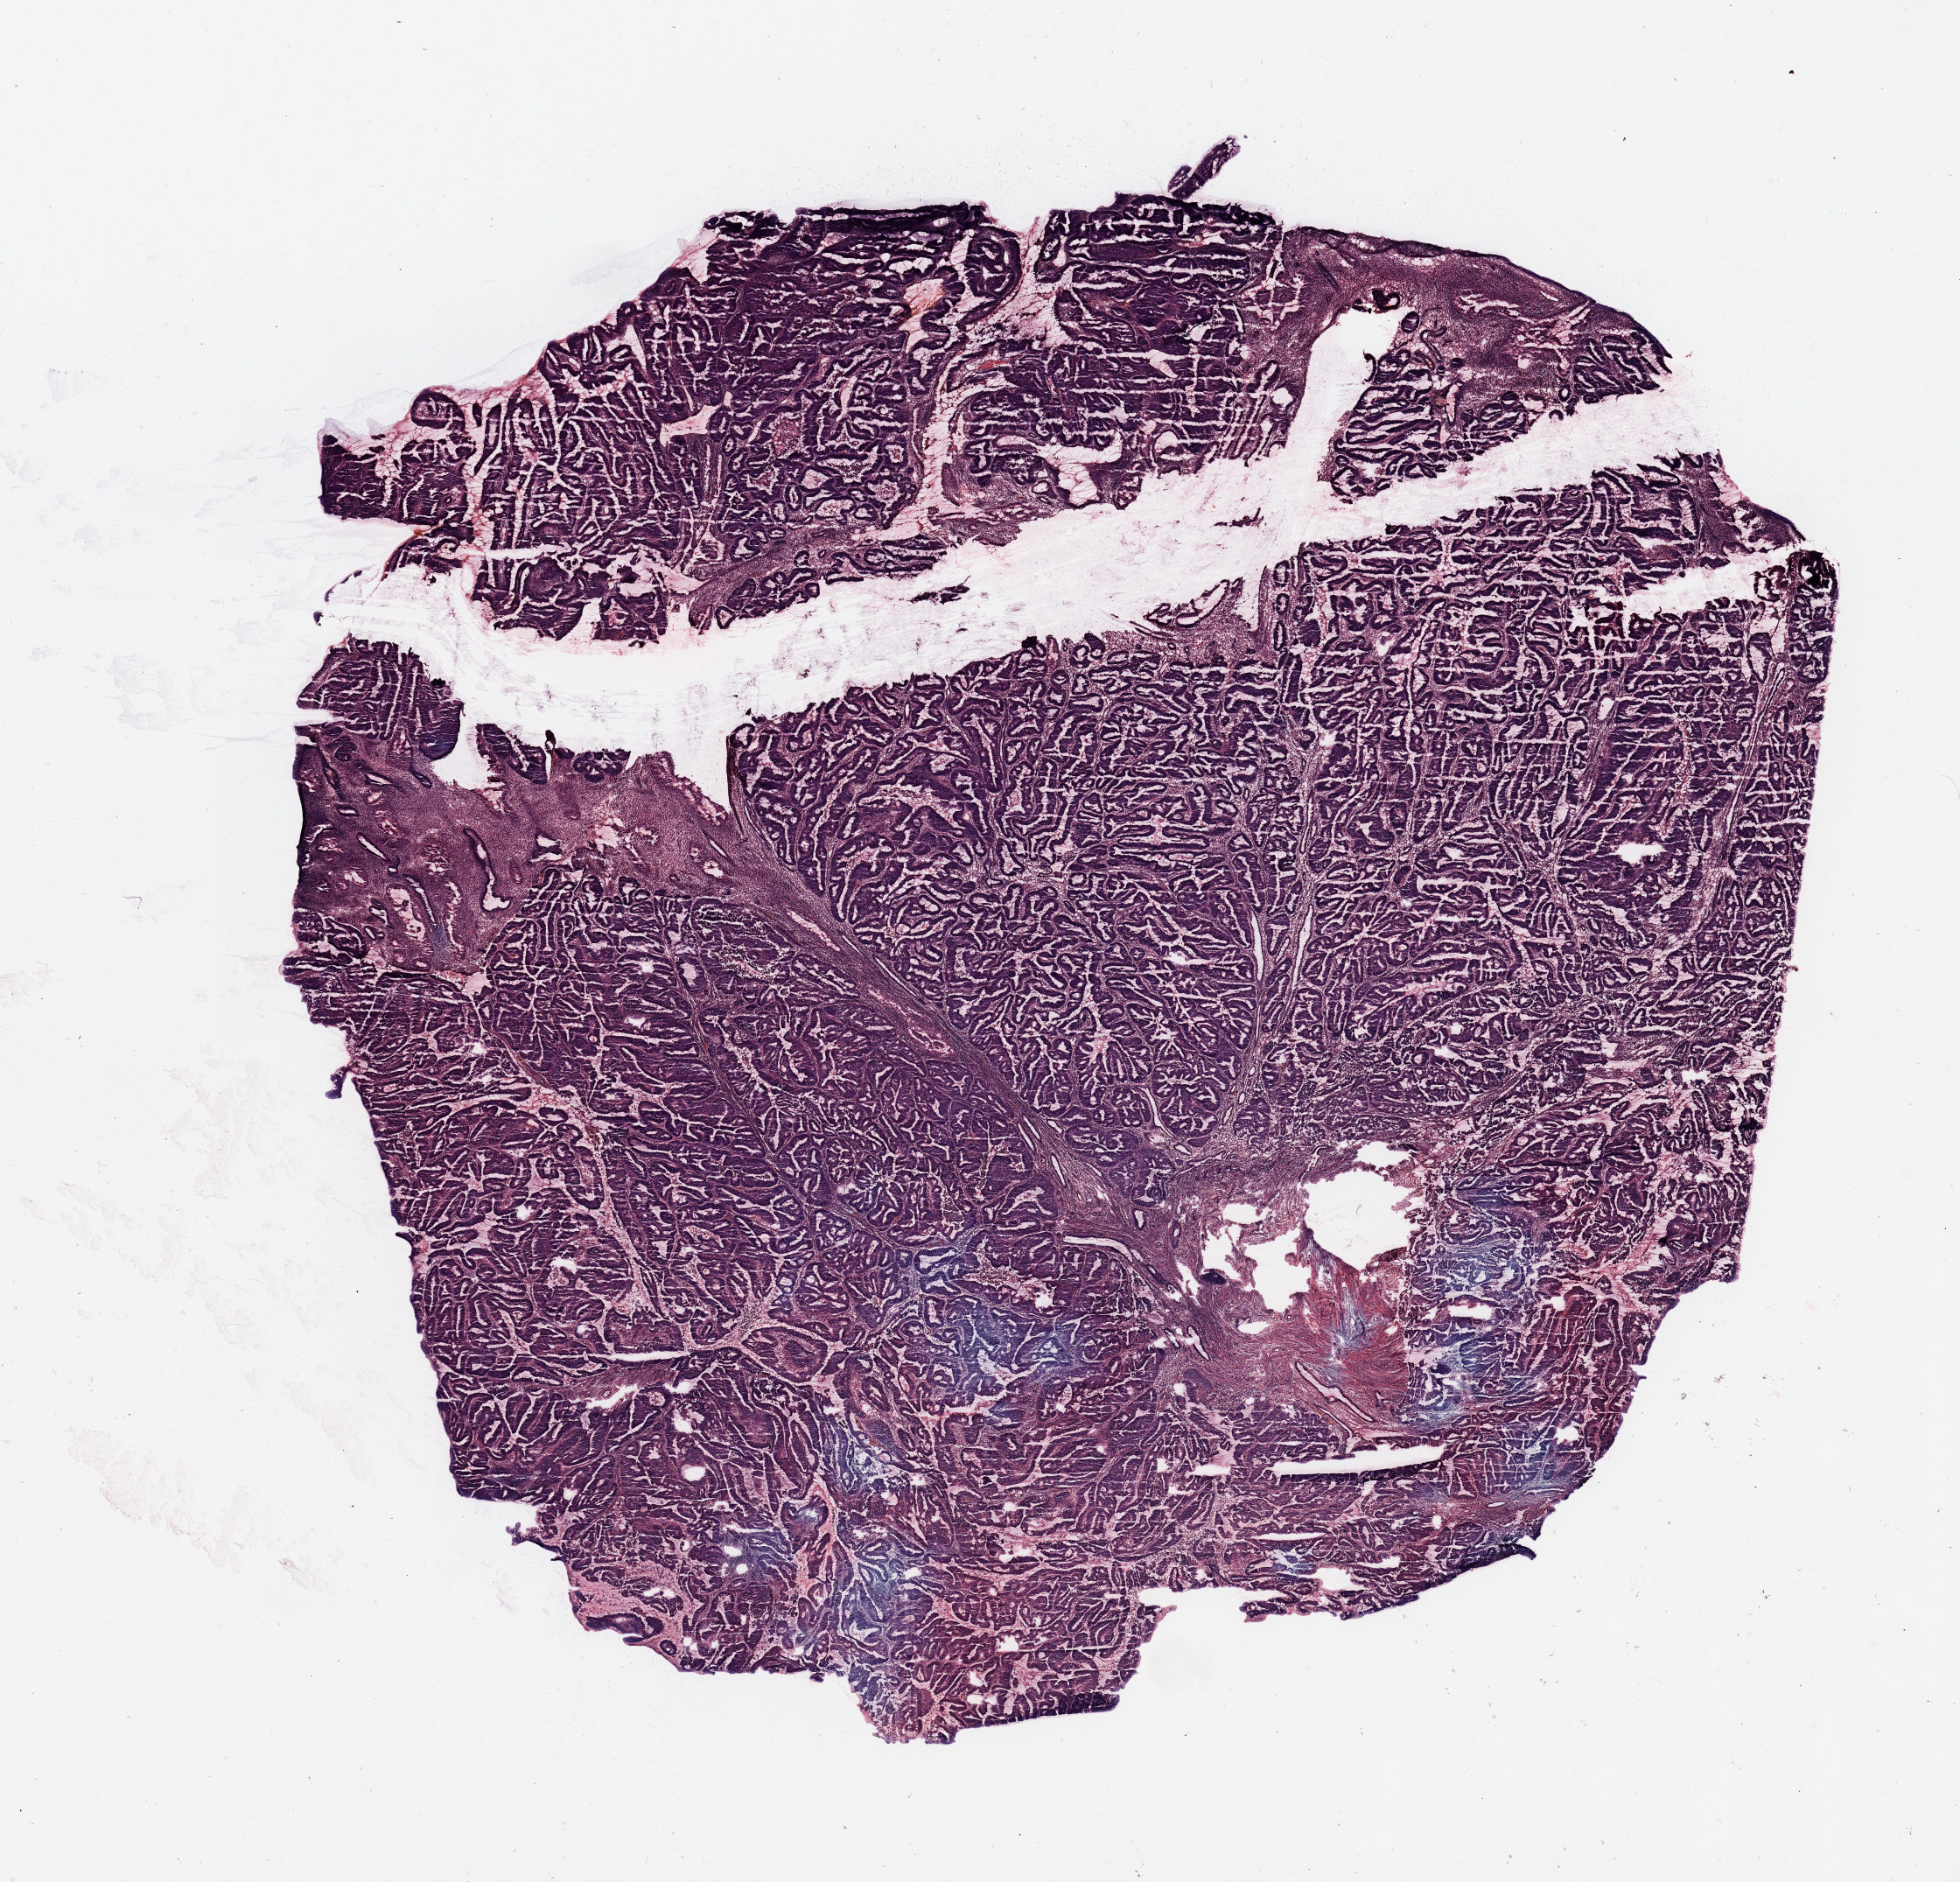
Hematoxylin and eosin (H&E) stained whole-slide image, whole scanned area (about 17.7 x 17.0 mm, acquisition: 20x scan) shown as a low-resolution overview, tumour tissue sample, sampled site: uterus. 45-year-old female patient. Histologic grade: G1 (well differentiated). Composition of this section per pathologist review: tumour nuclei 90%, necrosis 0%.
Diagnosis: Endometrioid adenocarcinoma, NOS. AJCC pathologic stage: I.